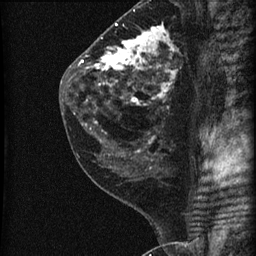
Breast MRI (dynamic contrast-enhanced), one sagittal slice; position 30 of 60 along the scan axis; dynamic contrast-enhanced series, image 2 of 3 at this slice position (ordered by acquisition); 1.5 T; TE 4.2 ms, TR 22.7 ms; 1.8 mm slice thickness; 256 × 256 image matrix, field of view 180 × 180 mm. Female patient, age 45 years. Case-level facts recorded for this patient, not image findings: setting: breast cancer imaged before/during neoadjuvant chemotherapy; receptor status: HR-positive, HER2-negative.
Outlined on this slice (semi-automatic segmentation, software-assisted and operator-edited):
- analysis volume of interest (the breast-tissue region the enhancement analysis was run in; not a lesion): box from (x=74, y=11) to (x=205, y=140) px
- tumour enhancement mask (voxels above the 90 % enhancement threshold inside the analysis volume of interest): (x=81, y=24)–(x=177, y=139)